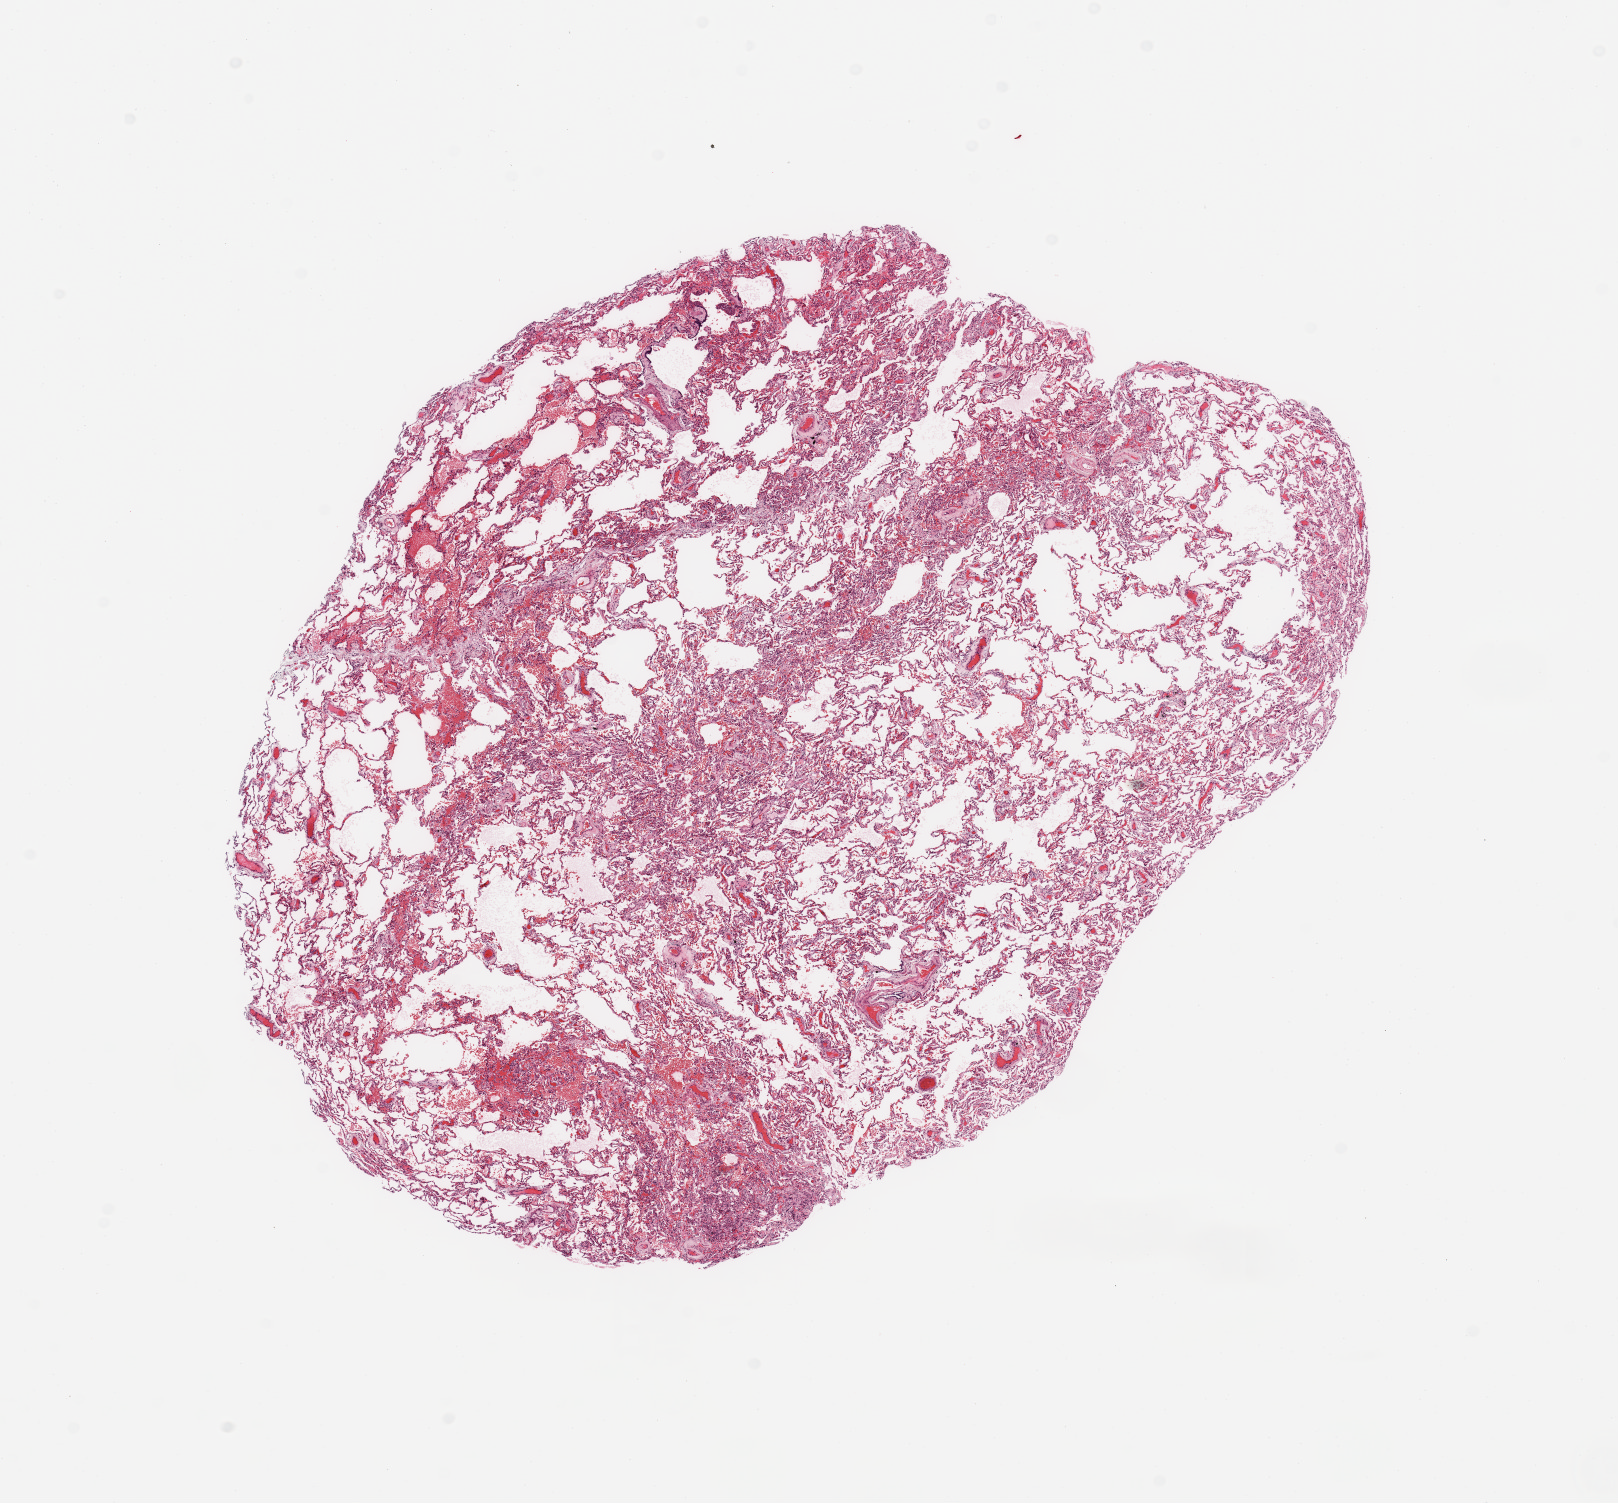
H&E whole-slide image — whole scanned area (about 12.8 x 11.9 mm) shown as a low-resolution overview, normal (non-tumour) tissue sample, sampled site: lung. Patient: male, age 71 years.
This section: normal (non-tumour) tissue from the same patient. Patient diagnosis: Adenocarcinoma, NOS.